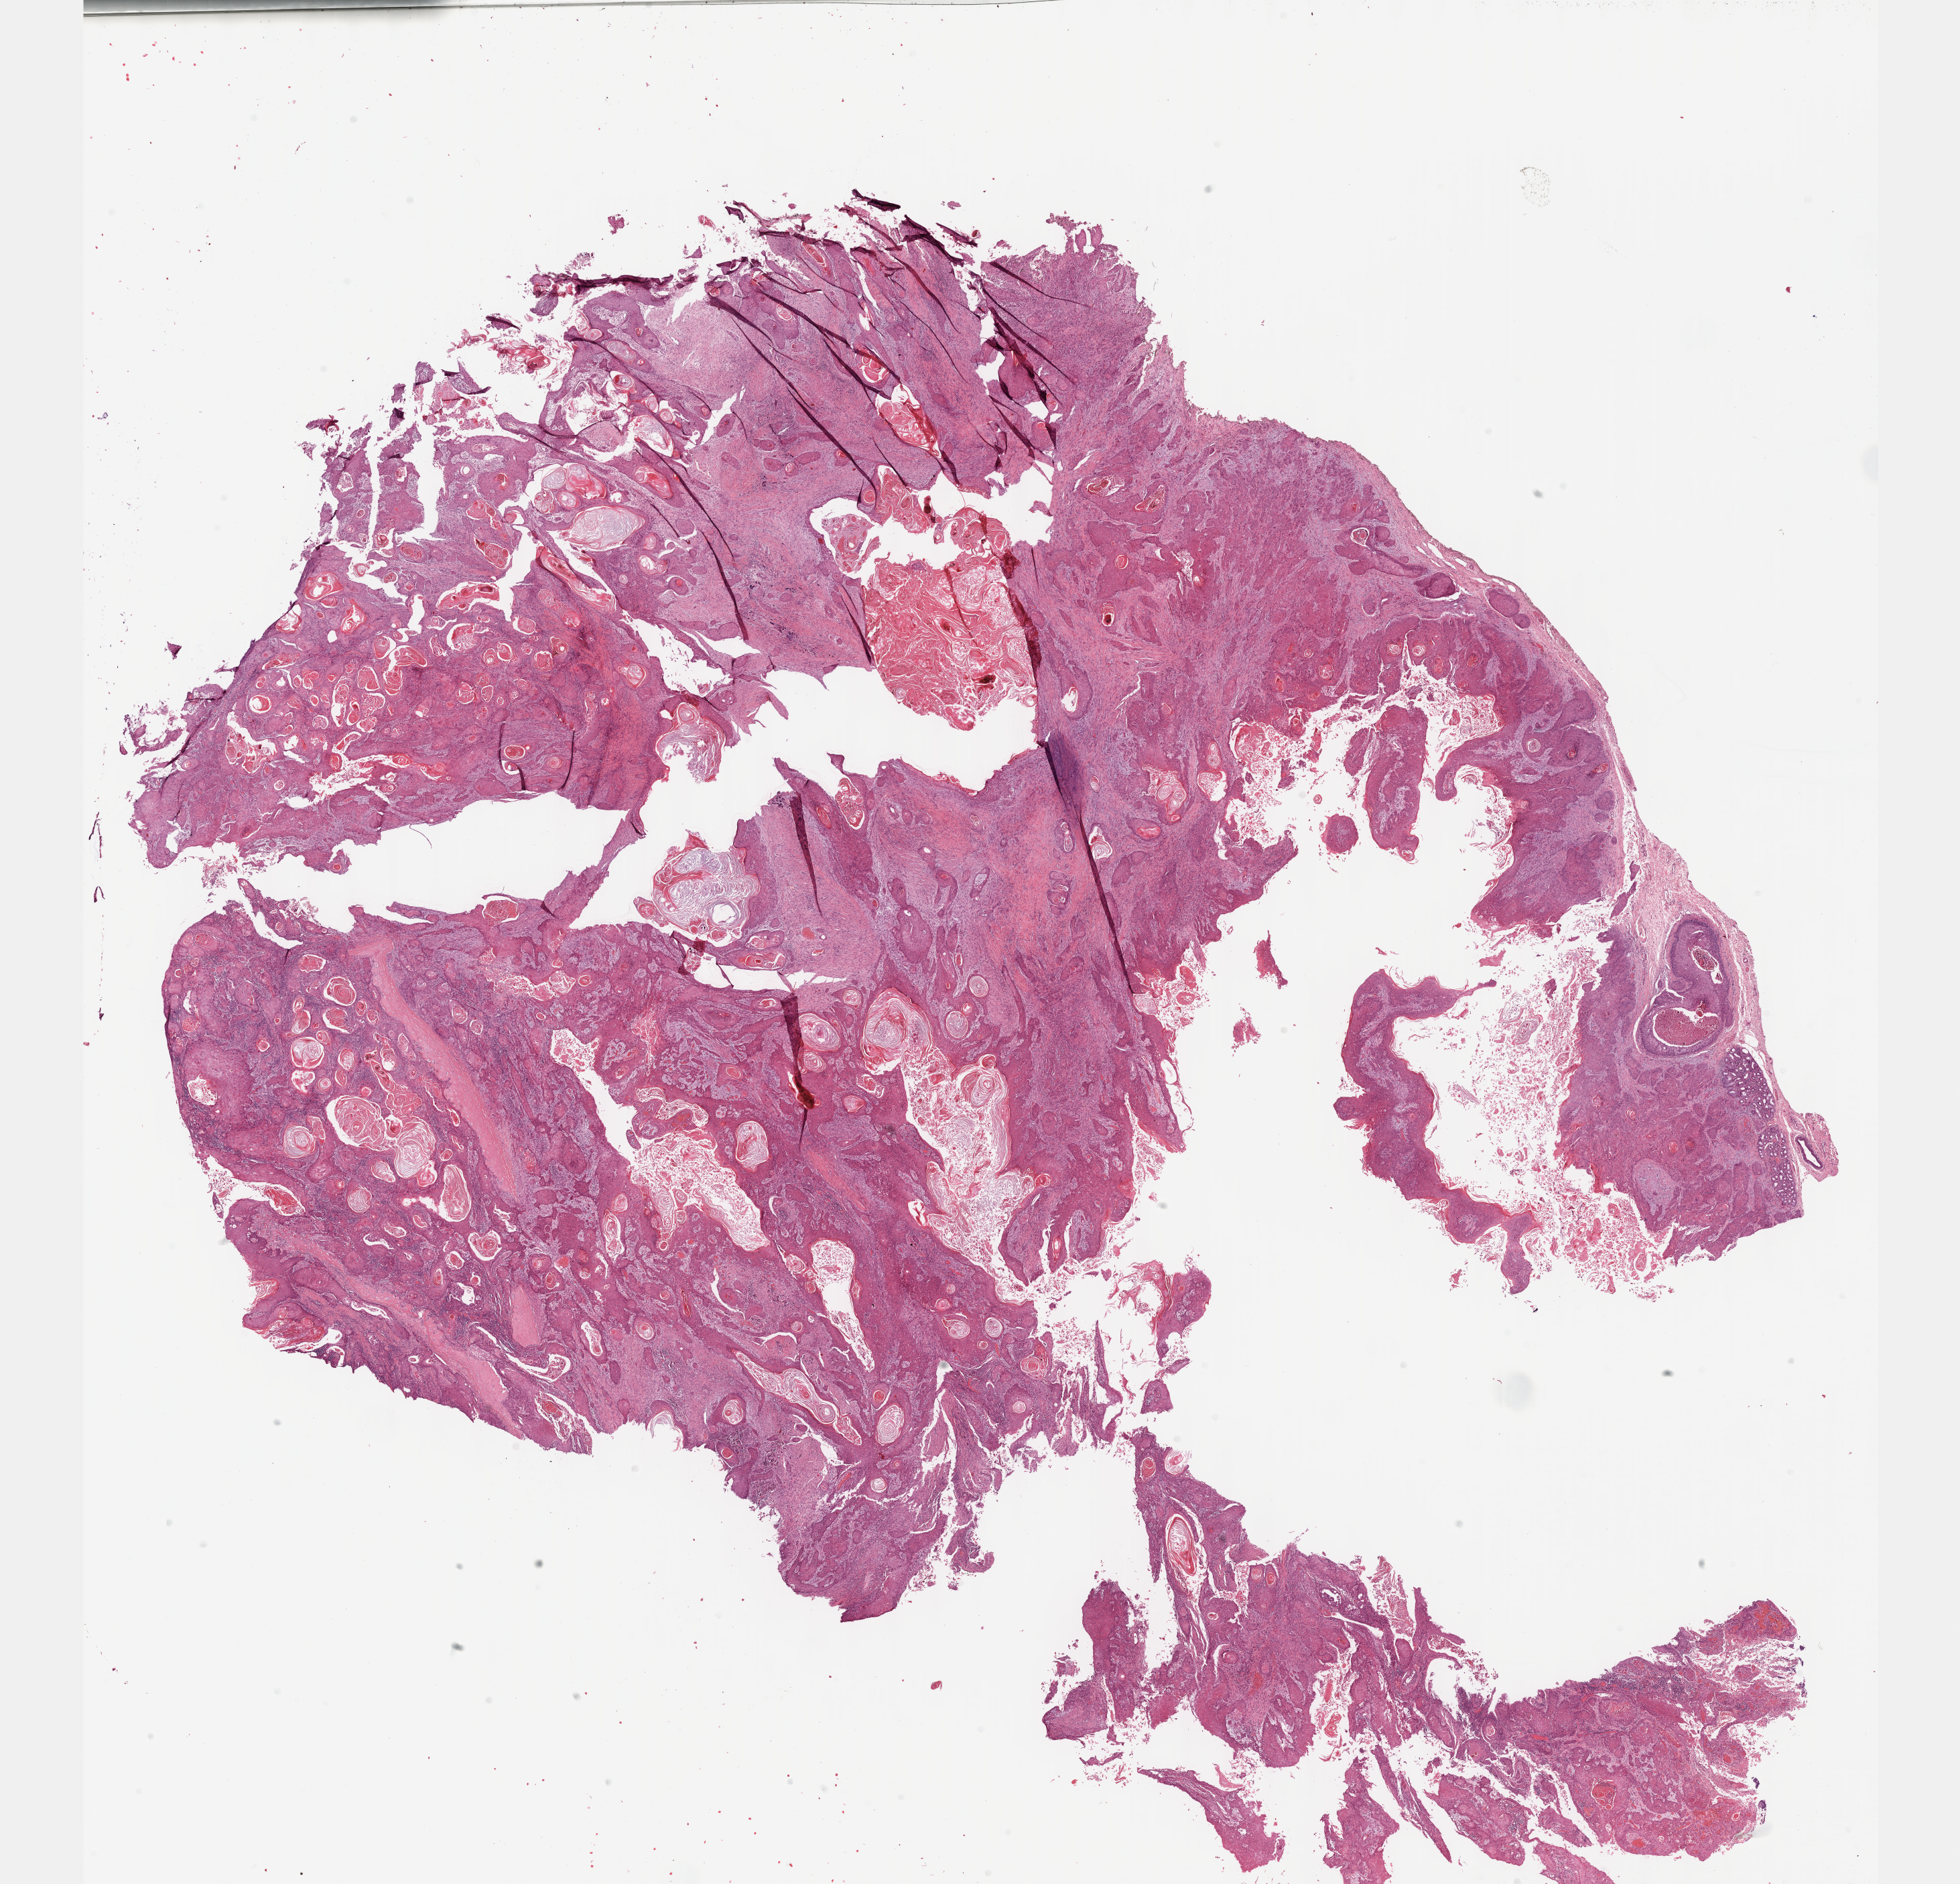
H&E-stained whole-slide image, whole scanned area (about 23.6 x 22.7 mm, from a 40x scan) shown as a low-resolution overview, formalin-fixed paraffin-embedded (FFPE) diagnostic section, head and neck, primary tumour sample. Patient: male, age at initial diagnosis 59 years. Histologic grade: G2 (moderately differentiated).
* AJCC pathologic stage: IVA (7th edition)
* pathologic diagnosis: Squamous cell carcinoma, keratinizing, NOS (larynx, NOS)